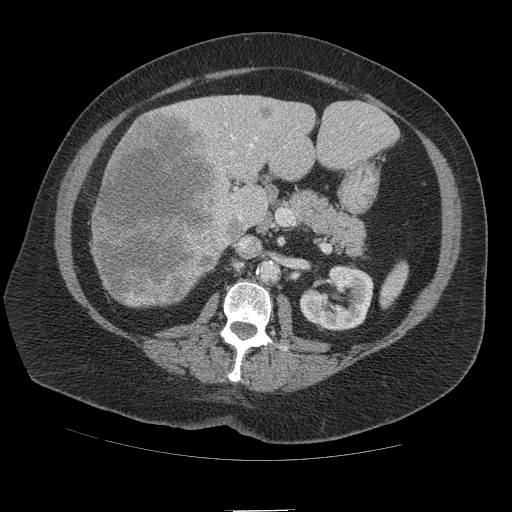
Contrast-enhanced abdominal CT (liver protocol), one axial slice; position 48 of 109 along the scan axis; 140 kVp; soft-tissue window (W 400 / L 40 HU); 2.5 mm slice thickness; 512 × 512 image matrix, field of view 420 × 420 mm. From the clinical record (not read from this slice): diagnosis: hepatocellular carcinoma (patient treated with transarterial chemoembolisation; whether this scan precedes or follows treatment is not stated here); TNM stage (as recorded): Stage-IVB; Child-Pugh class: A; tumour differentiation: poorly differentiated; tumour nodularity: multinodular.
Structures marked on this image (semi-automatic segmentation, software-assisted and operator-edited):
- liver parenchyma outside the tumour (the mass and vessels are separate outlines, so this box may not span the whole liver): box from (x=92, y=94) to (x=392, y=306) px
- mass: (x=90, y=105)–(x=238, y=307)
- liver vessels: (x=225, y=123)–(x=258, y=220)